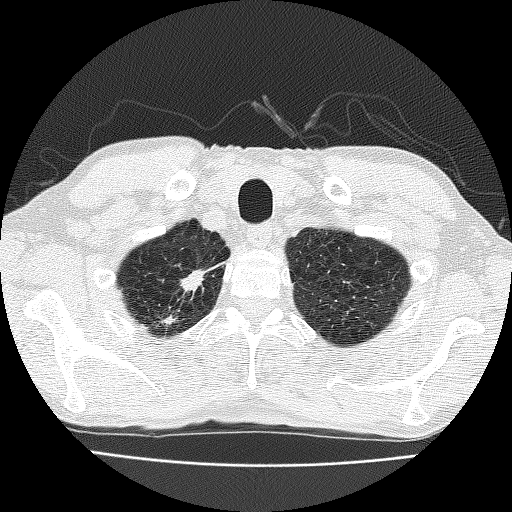
Axial slice from a low-dose chest CT screening exam, third annual screen, lung window (W 1500 / L -600 HU), 2 mm slice thickness, lung (sharp) reconstruction kernel (FC51). Male, age 63 years at enrolment. Current smoker at enrolment.
Lesion marked by an expert reader, bounding box [x1, y1, x2, y2] px = [145, 257, 225, 331]. The exam's reader record, not a measurement of the box and not confirmed to be the same lesion: non-calcified nodule or mass ≥4 mm, right upper lobe, 17 × 10 mm, spiculated (stellate) margins, soft tissue attenuation, pre-existing on the prior screen: yes; interval growth: yes. Participant outcome: lung cancer diagnosed 28 days after this screen — adenocarcinoma, NOS, right upper lobe, moderately differentiated (G2), stage IIIB (AJCC 6th edition), 17 mm at pathology.